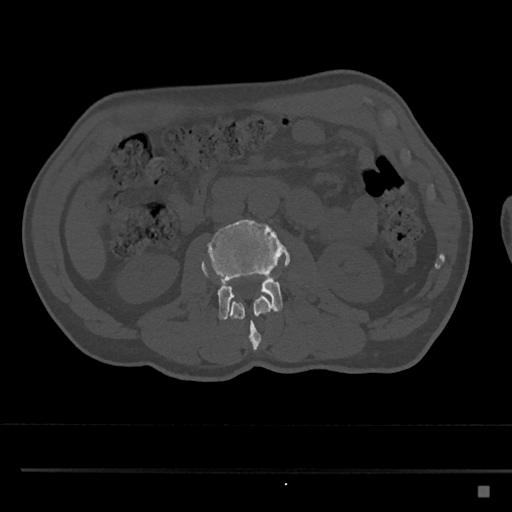
CT including the spine, one axial slice. Position 723 of 797 along the scan axis. Reconstruction kernel Br40s/3. Bone window (W 1800 / L 400 HU). 512 × 512 image matrix, field of view 391 × 391 mm. Patient: male, 59 years. Case-level facts recorded for this patient, not image findings: primary cancer: prostate.
Annotated regions visible in this slice (semi-automatically segmented with operator editing):
- L2 vertebra: bounding box (x1, y1, x2, y2) in pixels: (202, 264, 272, 350)
- L3 vertebra: (201, 219, 290, 320)